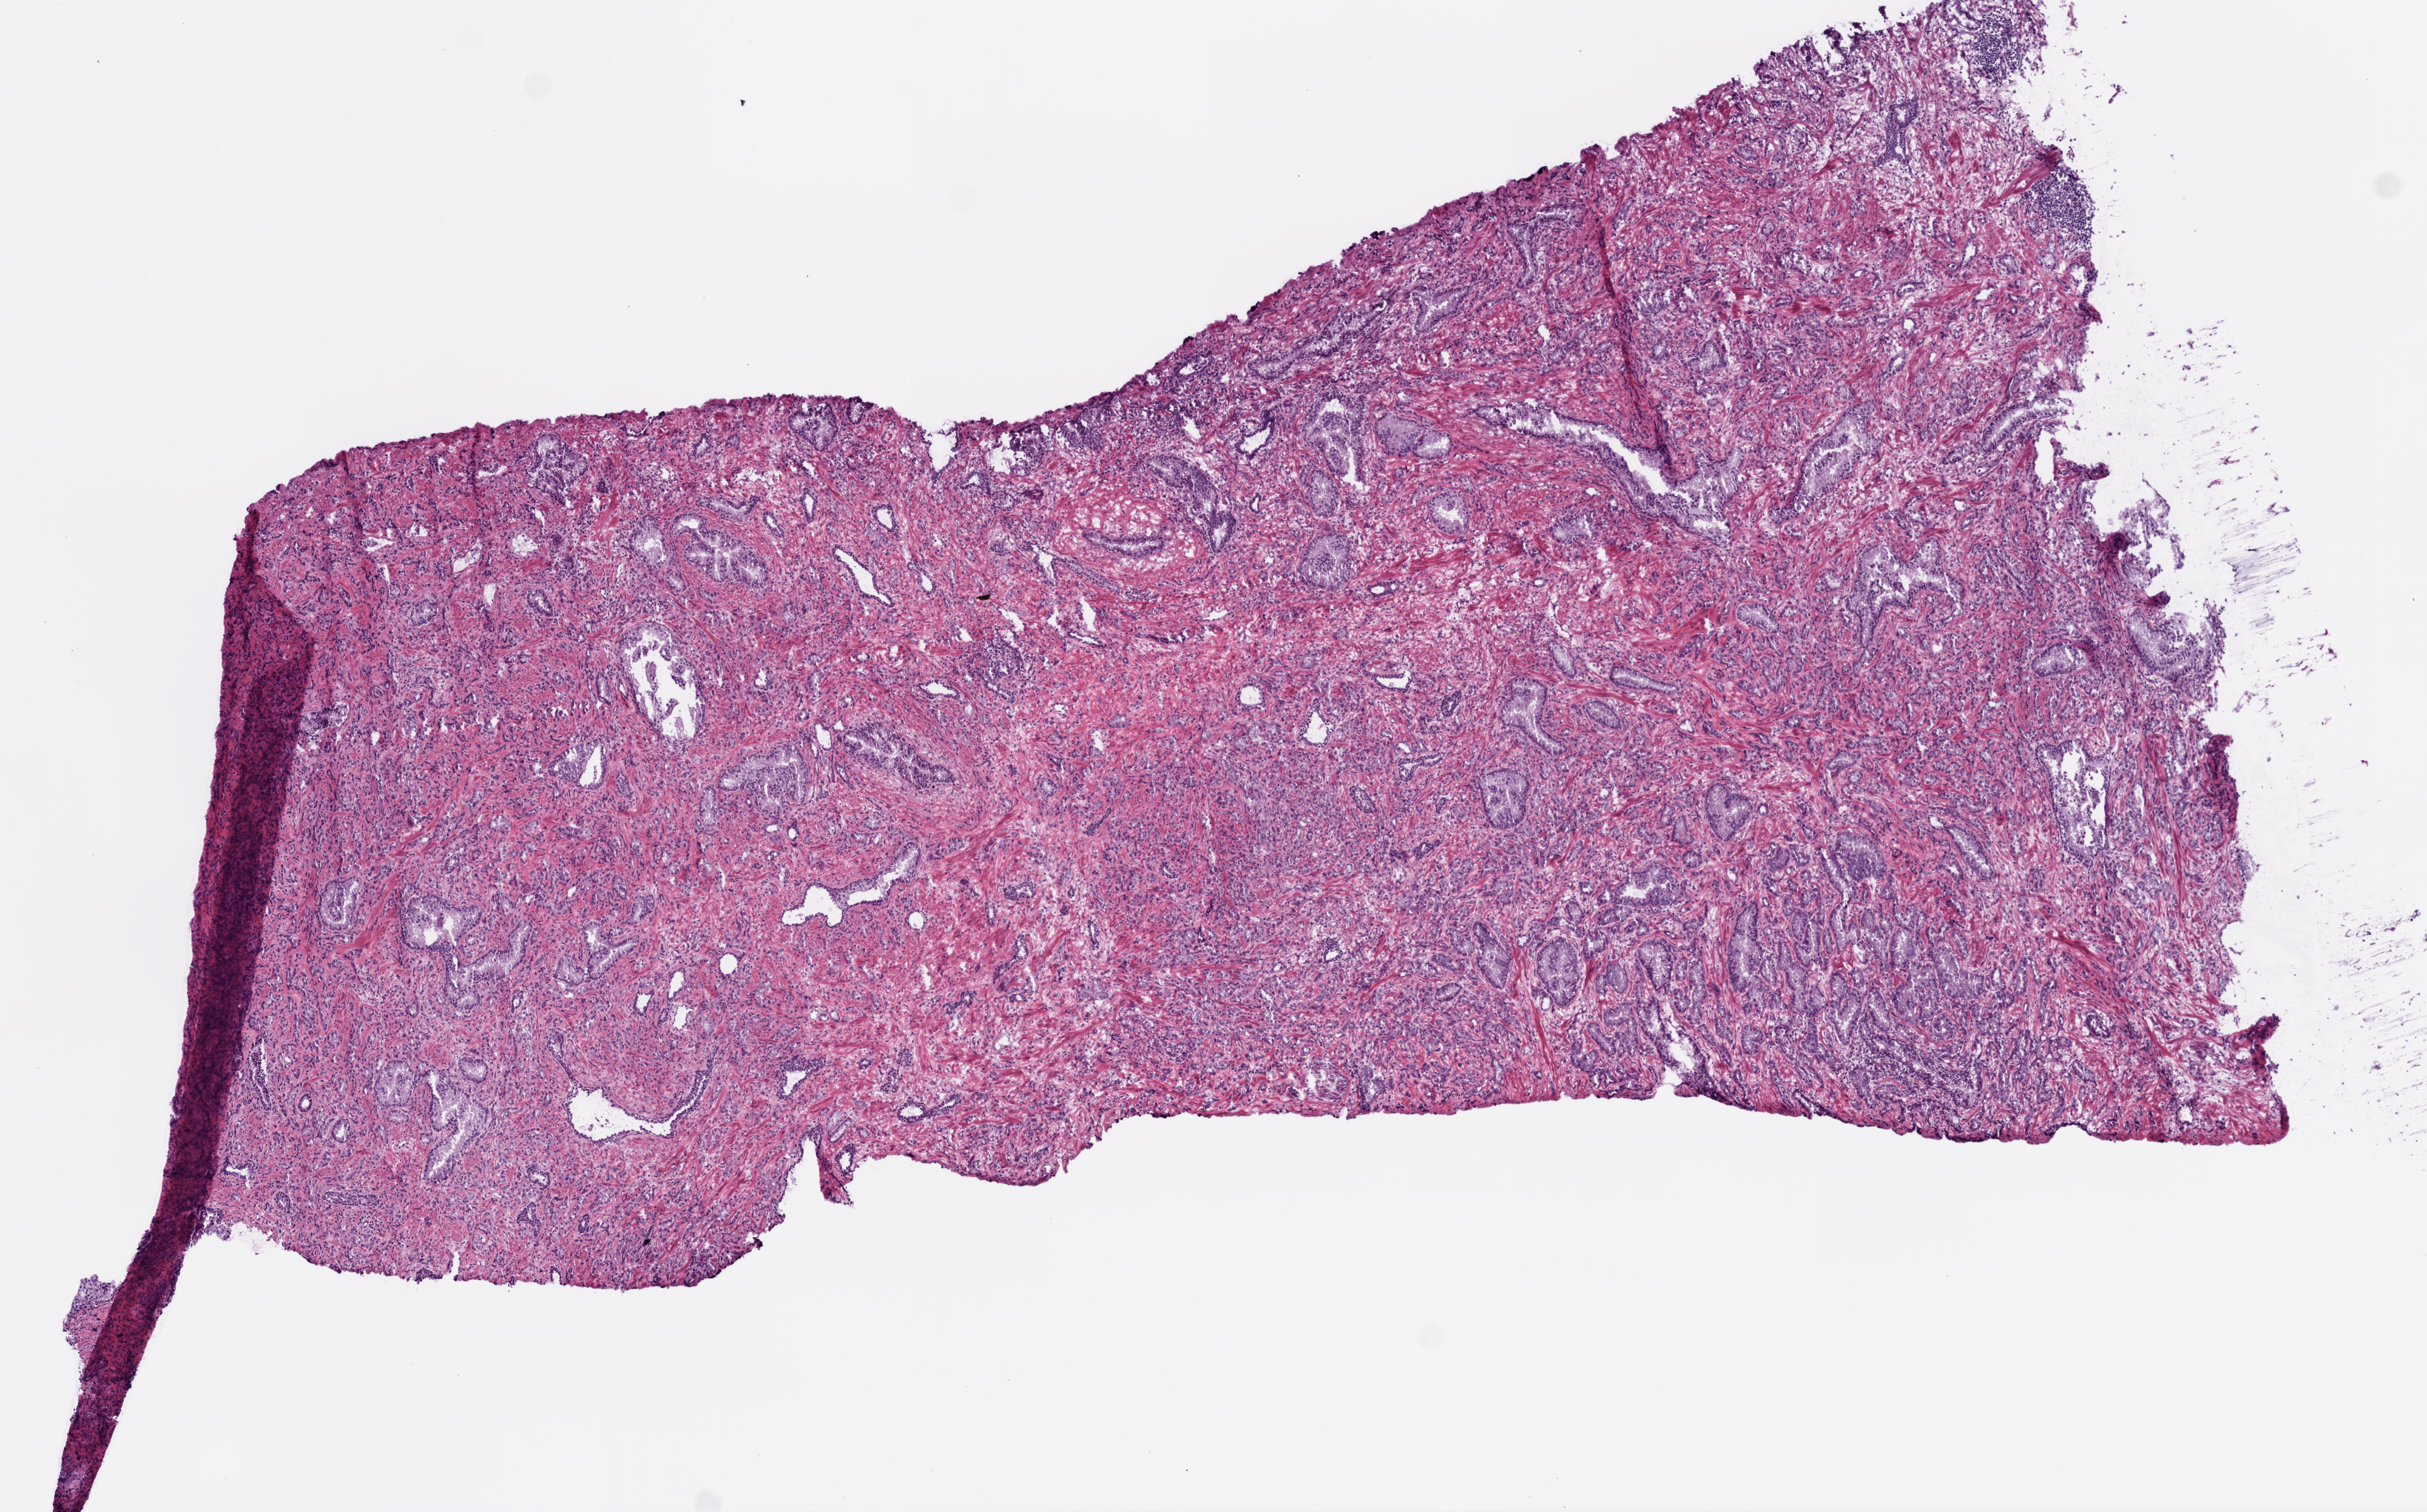
Digitized H&E tissue section (whole slide) — shown as a low-resolution overview of the whole scanned area (about 8.0 x 5.0 mm, slide scanned at 20x), frozen section from the bottom of the tissue portion, sample: primary tumour, prostate. Male, age 57 years at initial diagnosis. Gleason score: 9 (4+5). Slide review estimates, as recorded: tumour cells 55%, tumour nuclei 60%, normal cells 20%, stromal cells 25%, necrosis 0%. Inflammatory infiltration, as recorded: lymphocyte infiltration 4%, monocyte infiltration 2%, neutrophil infiltration 0%.
Pathologic diagnosis: Acinar cell carcinoma (prostate gland). Lymph nodes positive (case pathology): 0 of 6 examined.